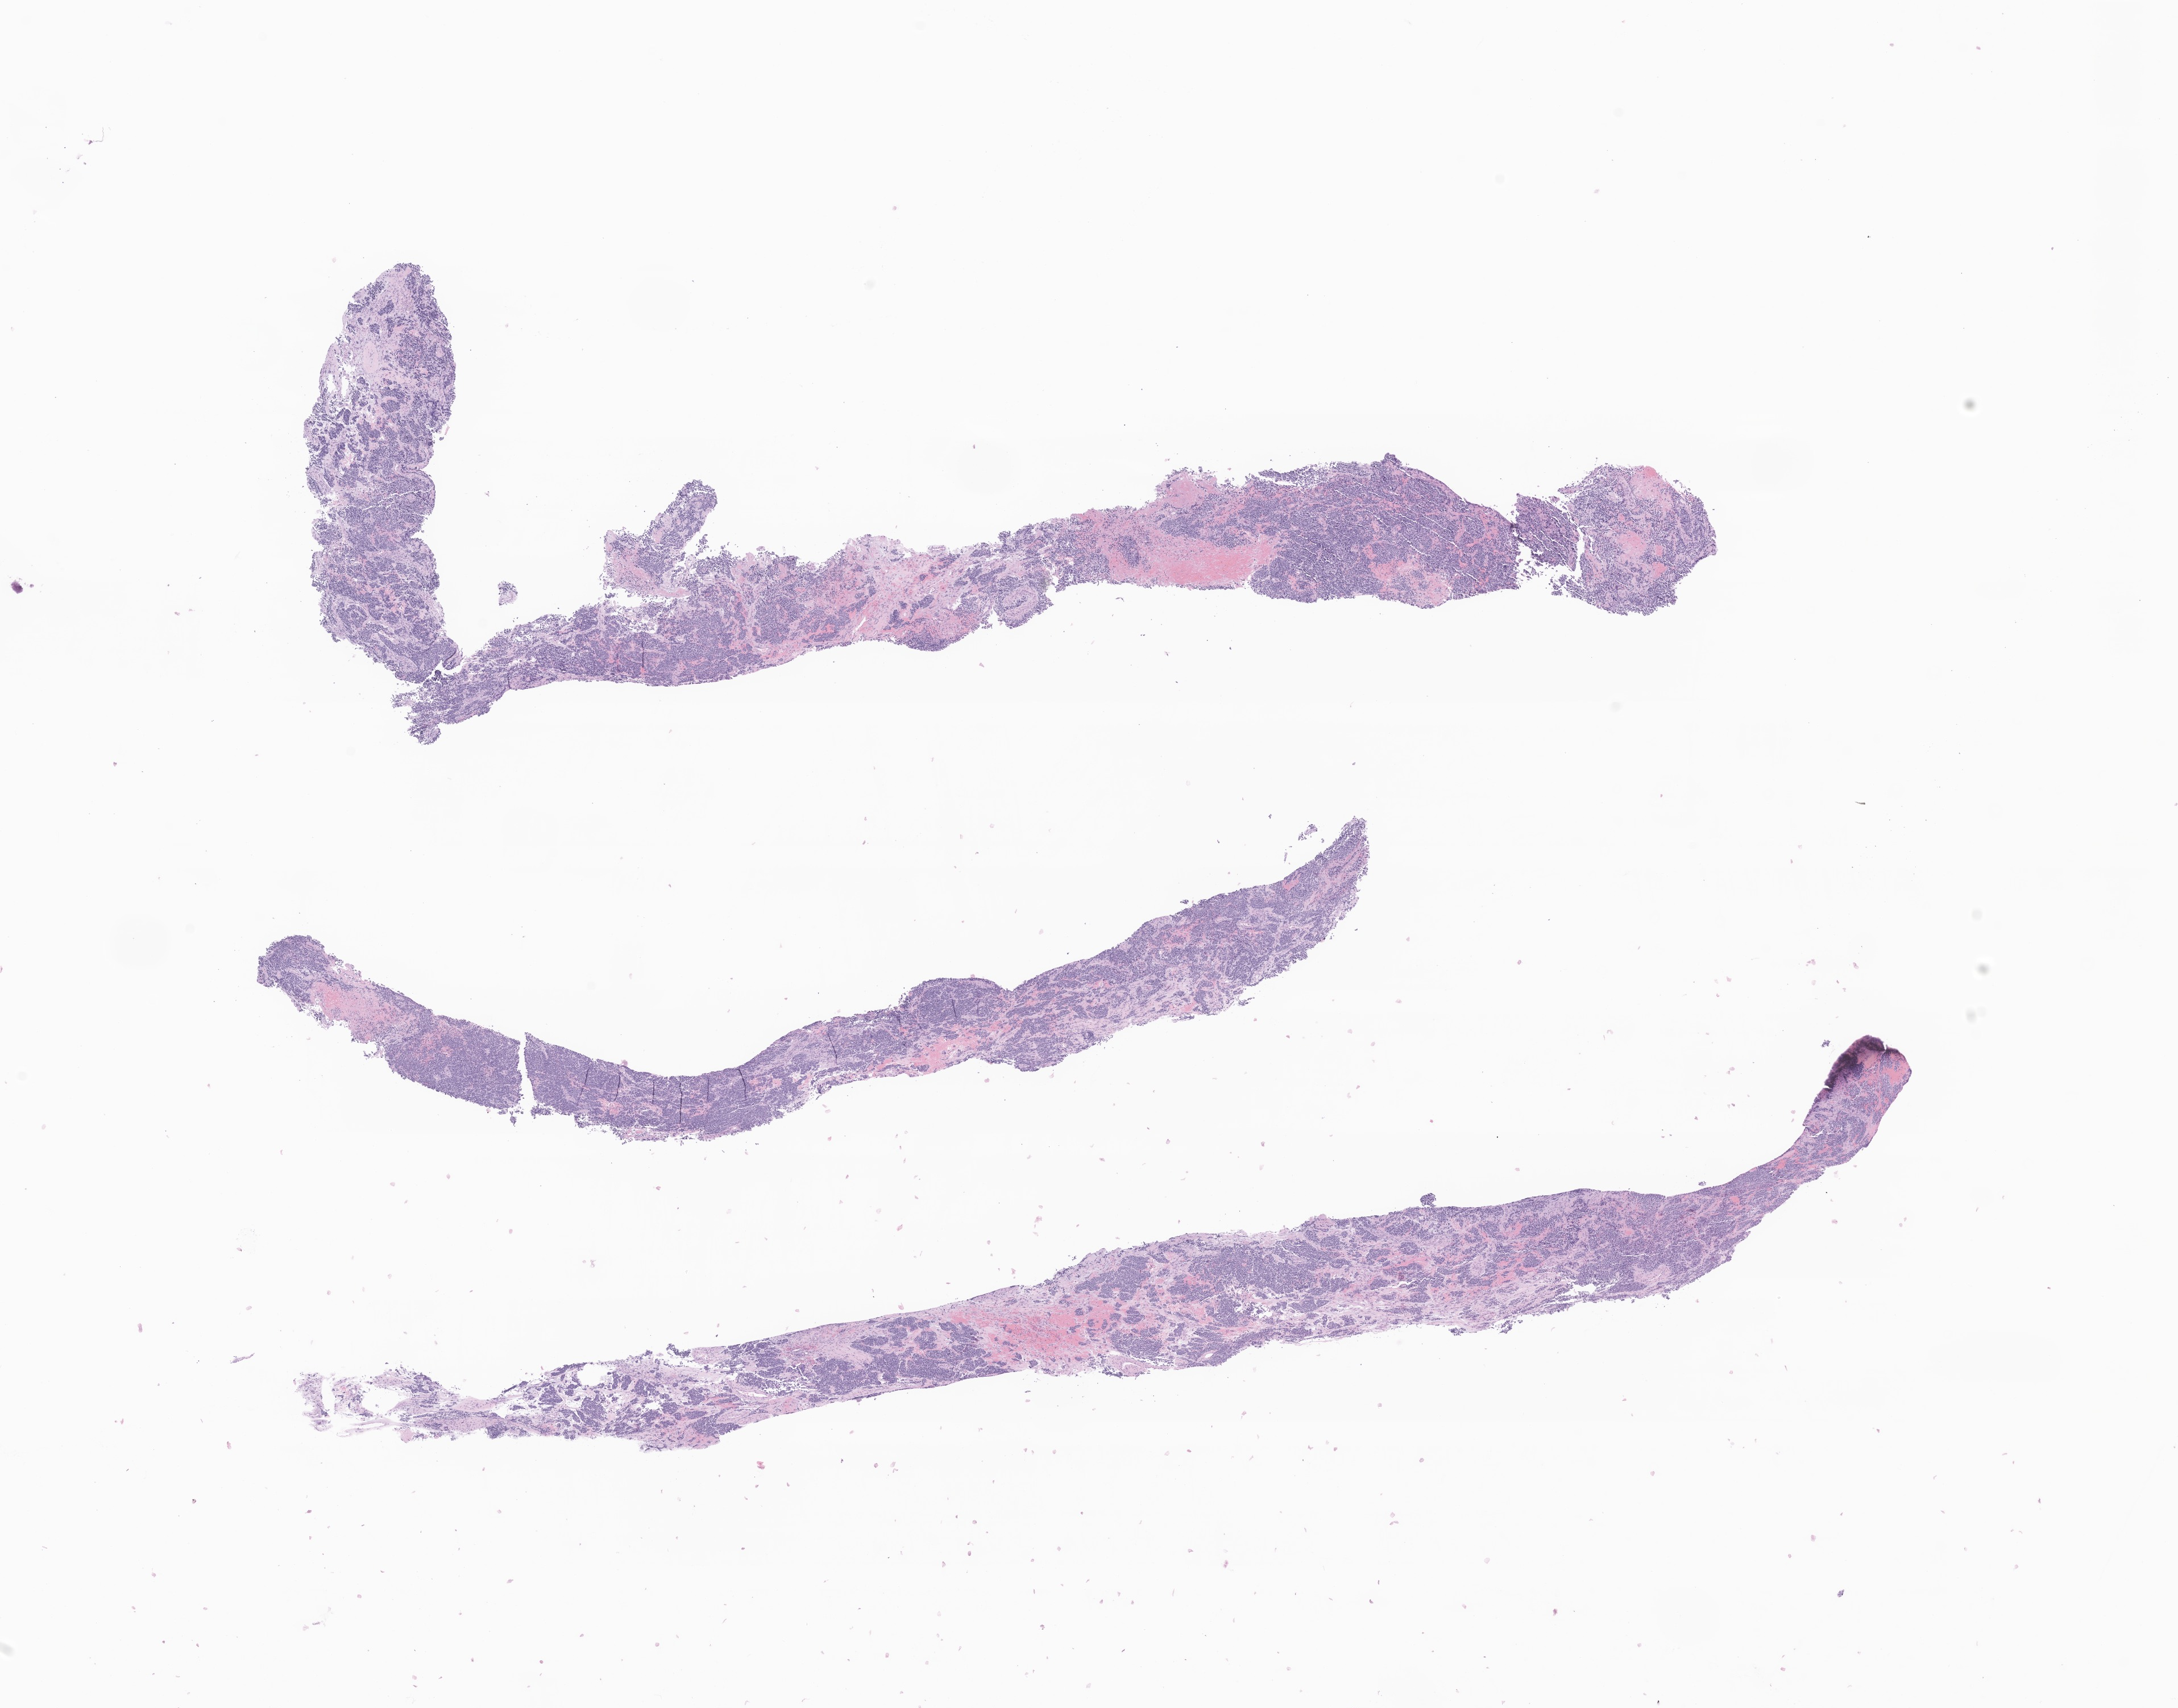
H&E whole-slide image of tumor tissue from the adrenal gland, whole scanned area (about 16.2 x 12.7 mm) shown as a low-resolution overview, formalin-fixed paraffin-embedded section. Patient male; age 554 days (about 1.5 years).
* recorded diagnosis: Neuroblastoma, NOS